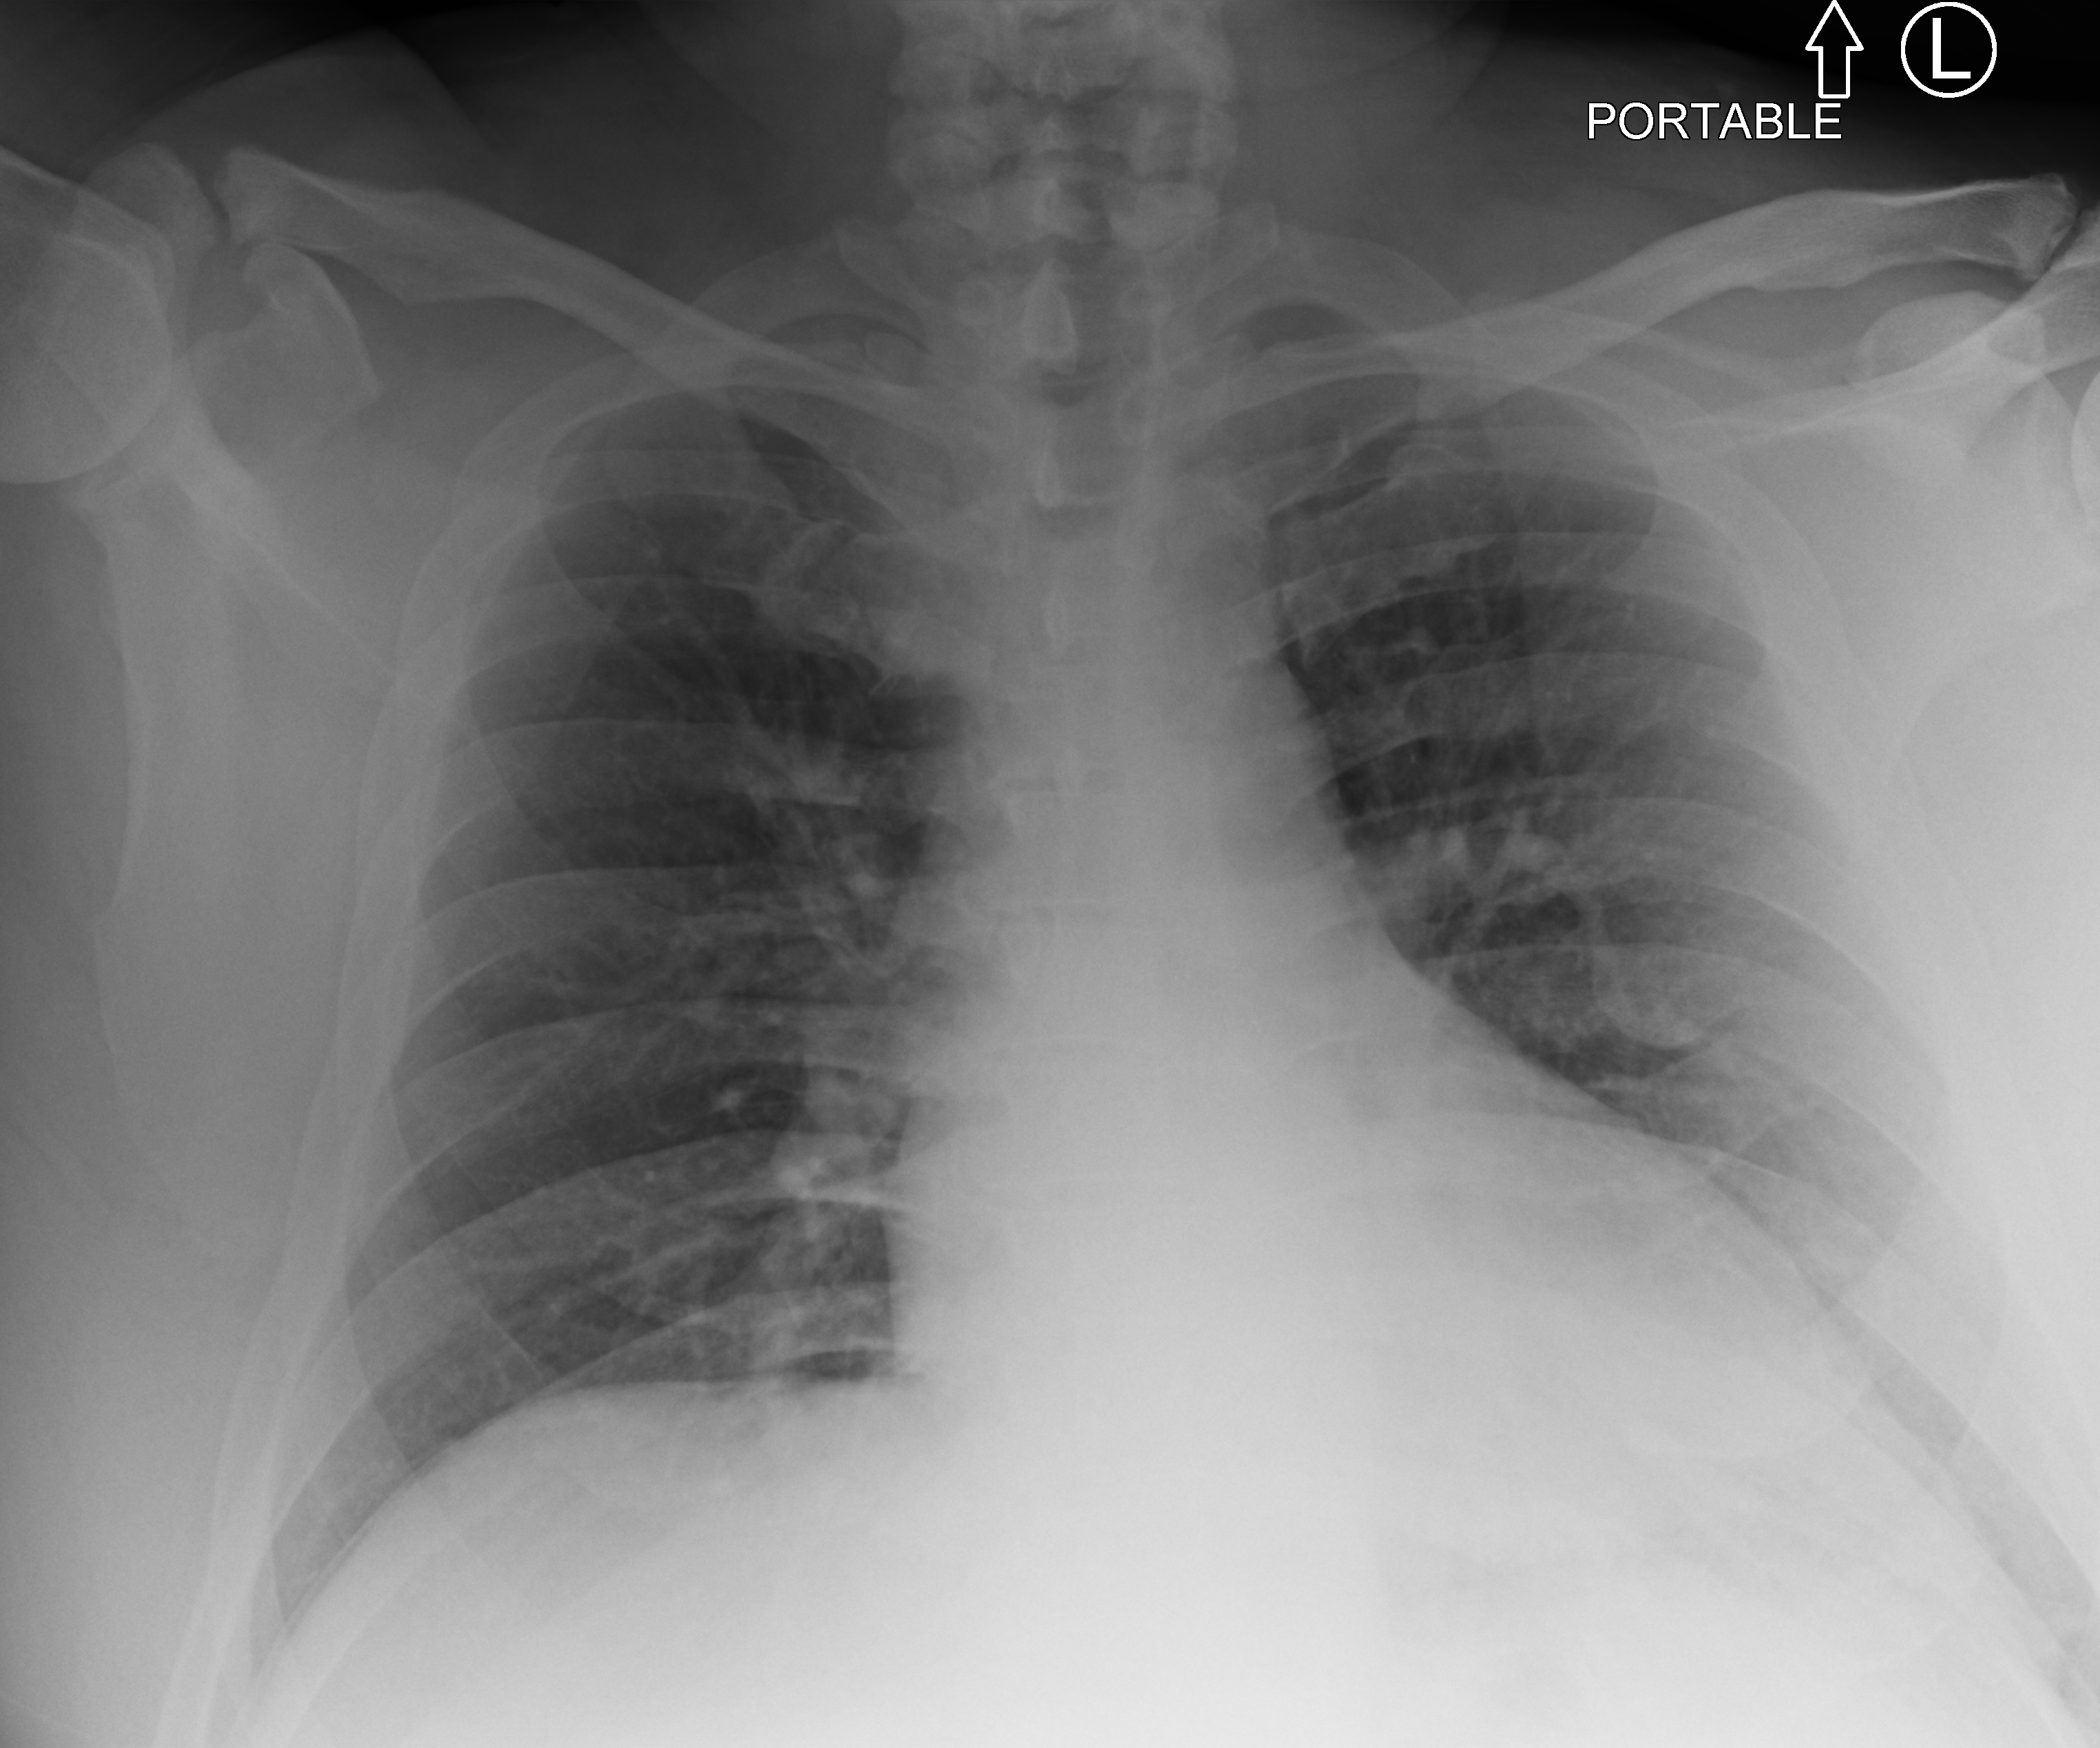
Chest X-ray (portable), anteroposterior (AP) projection. Male patient hospitalised with COVID-19, age 18–59 years.
From the hospital-stay record, not from the radiograph (when in the stay this image was taken is not recorded): admitted to intensive care during this hospital stay: no.